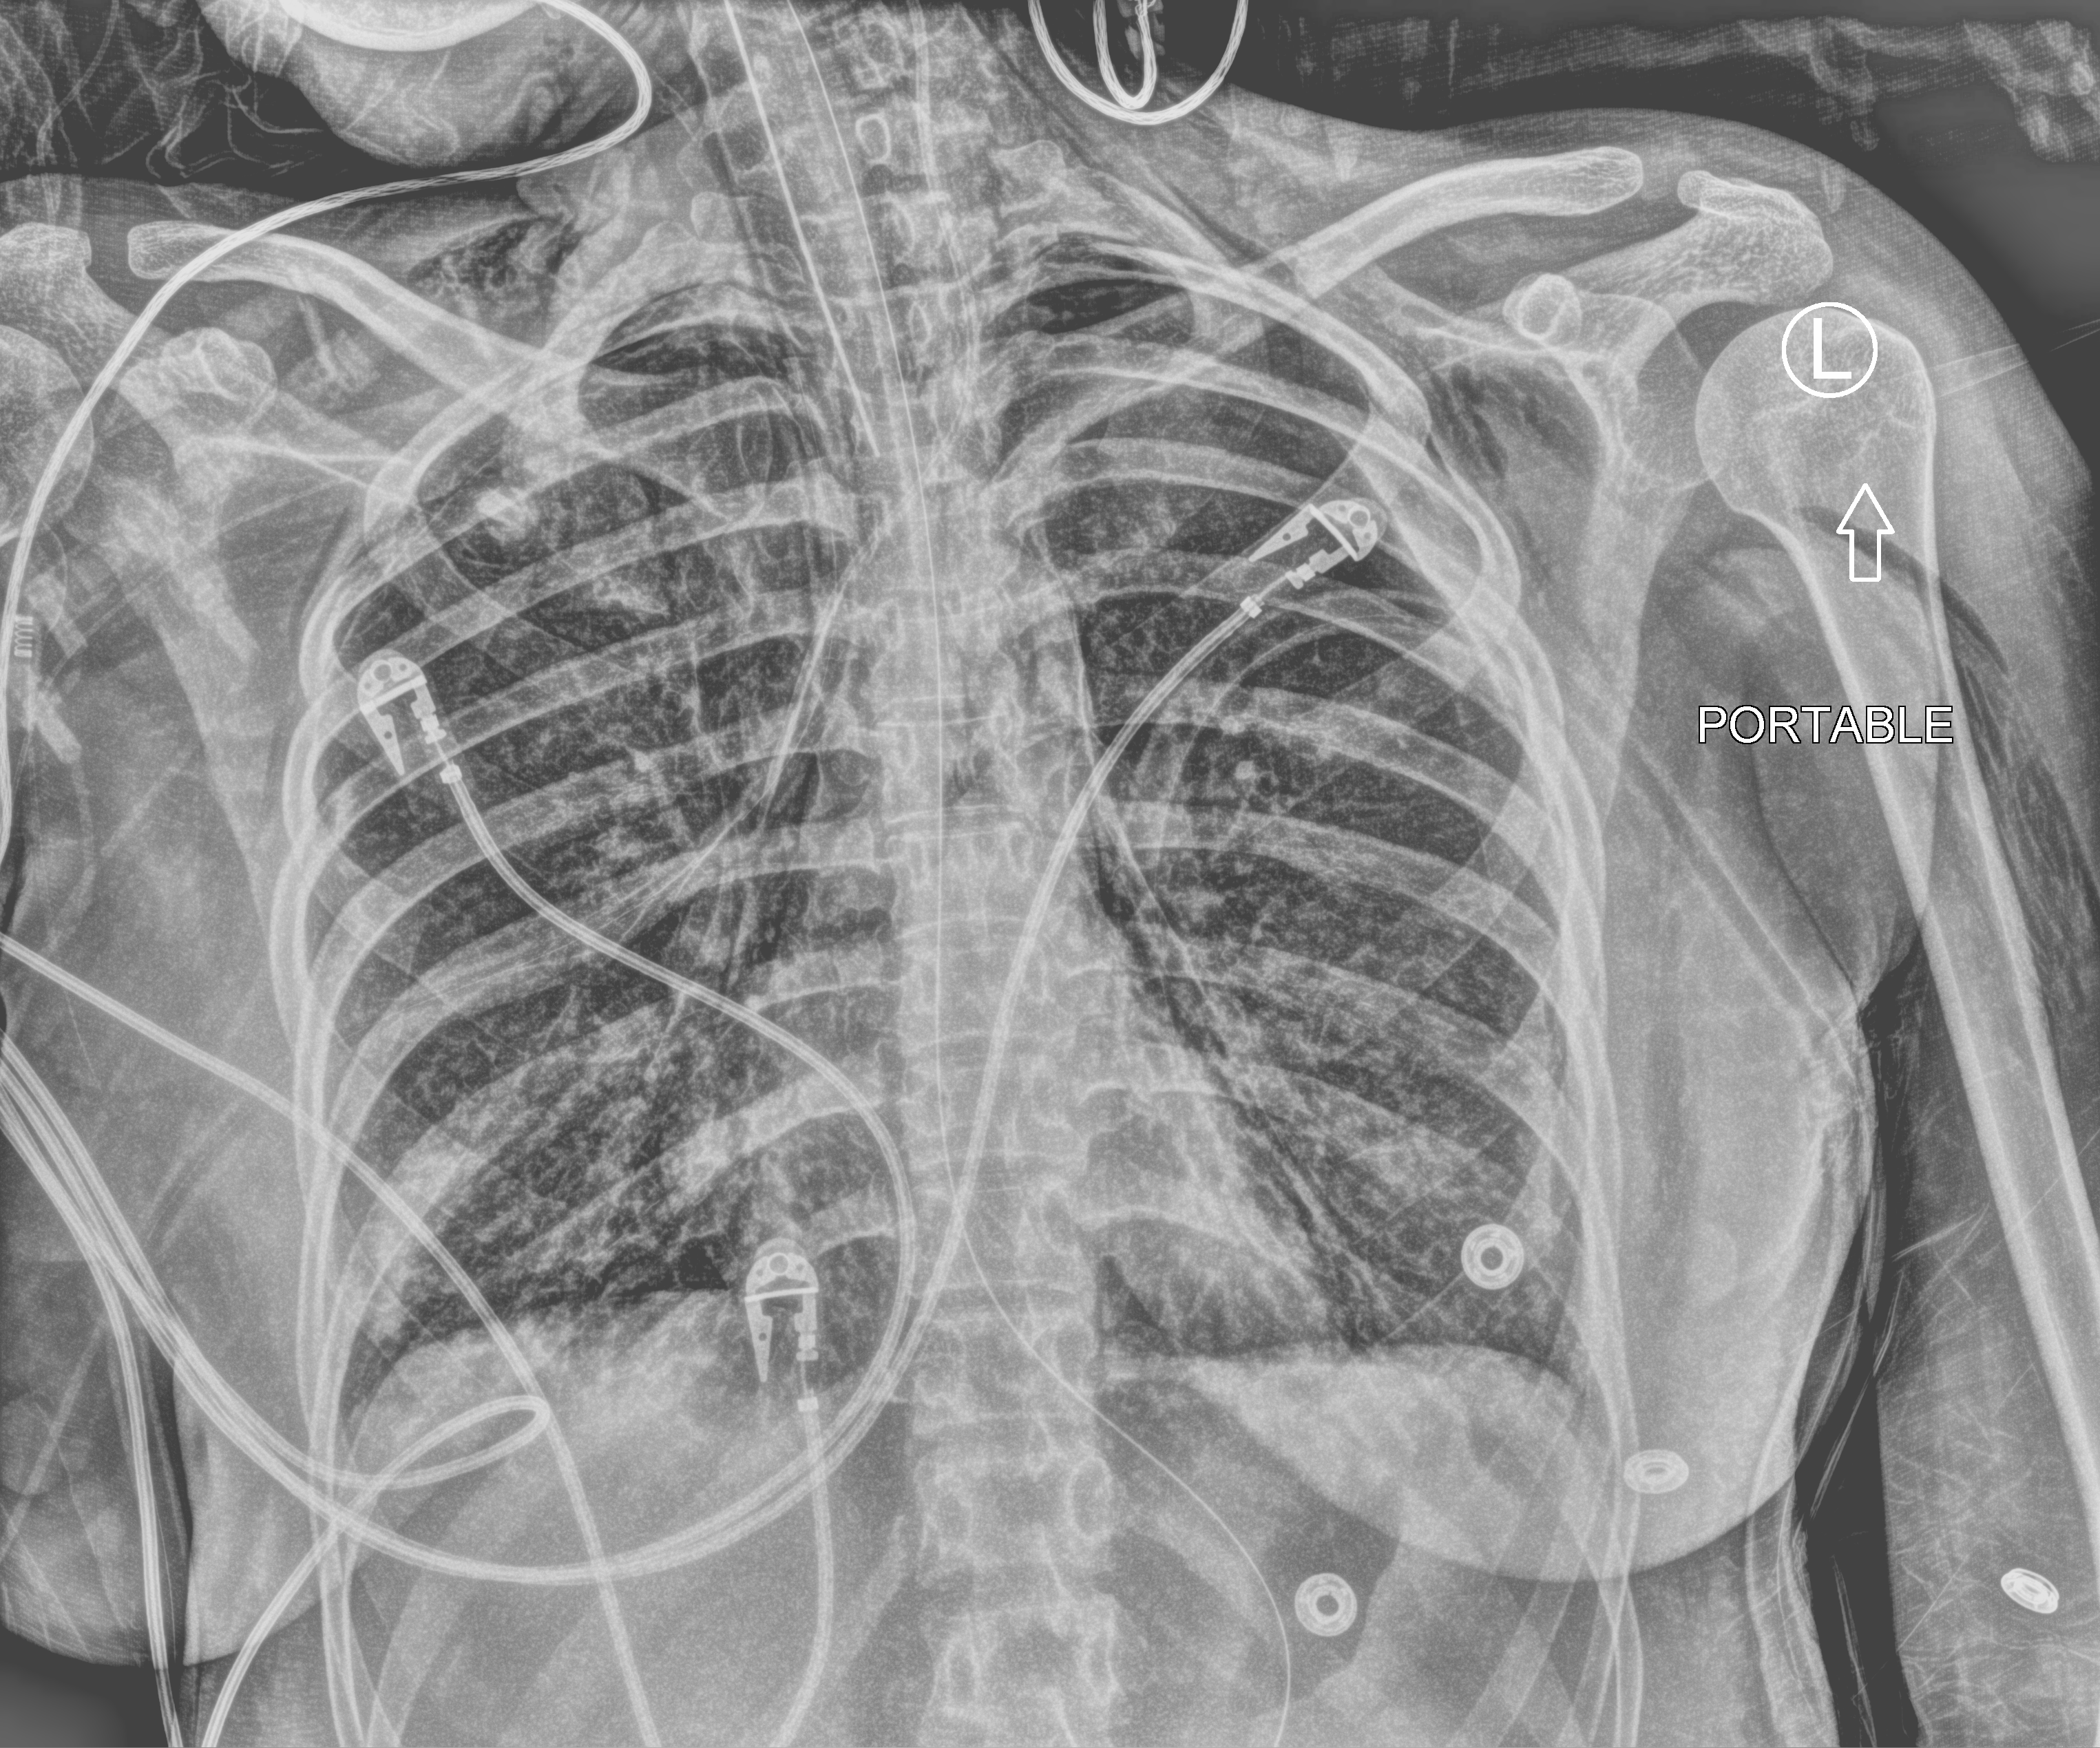
Bedside chest radiograph (computed radiography). Adult patient hospitalised with COVID-19, age 18–59 years.
From the hospital-stay record, not from the radiograph (when in the stay this image was taken is not recorded): length of hospital stay: 30 days; chronic kidney disease (admission record): no.